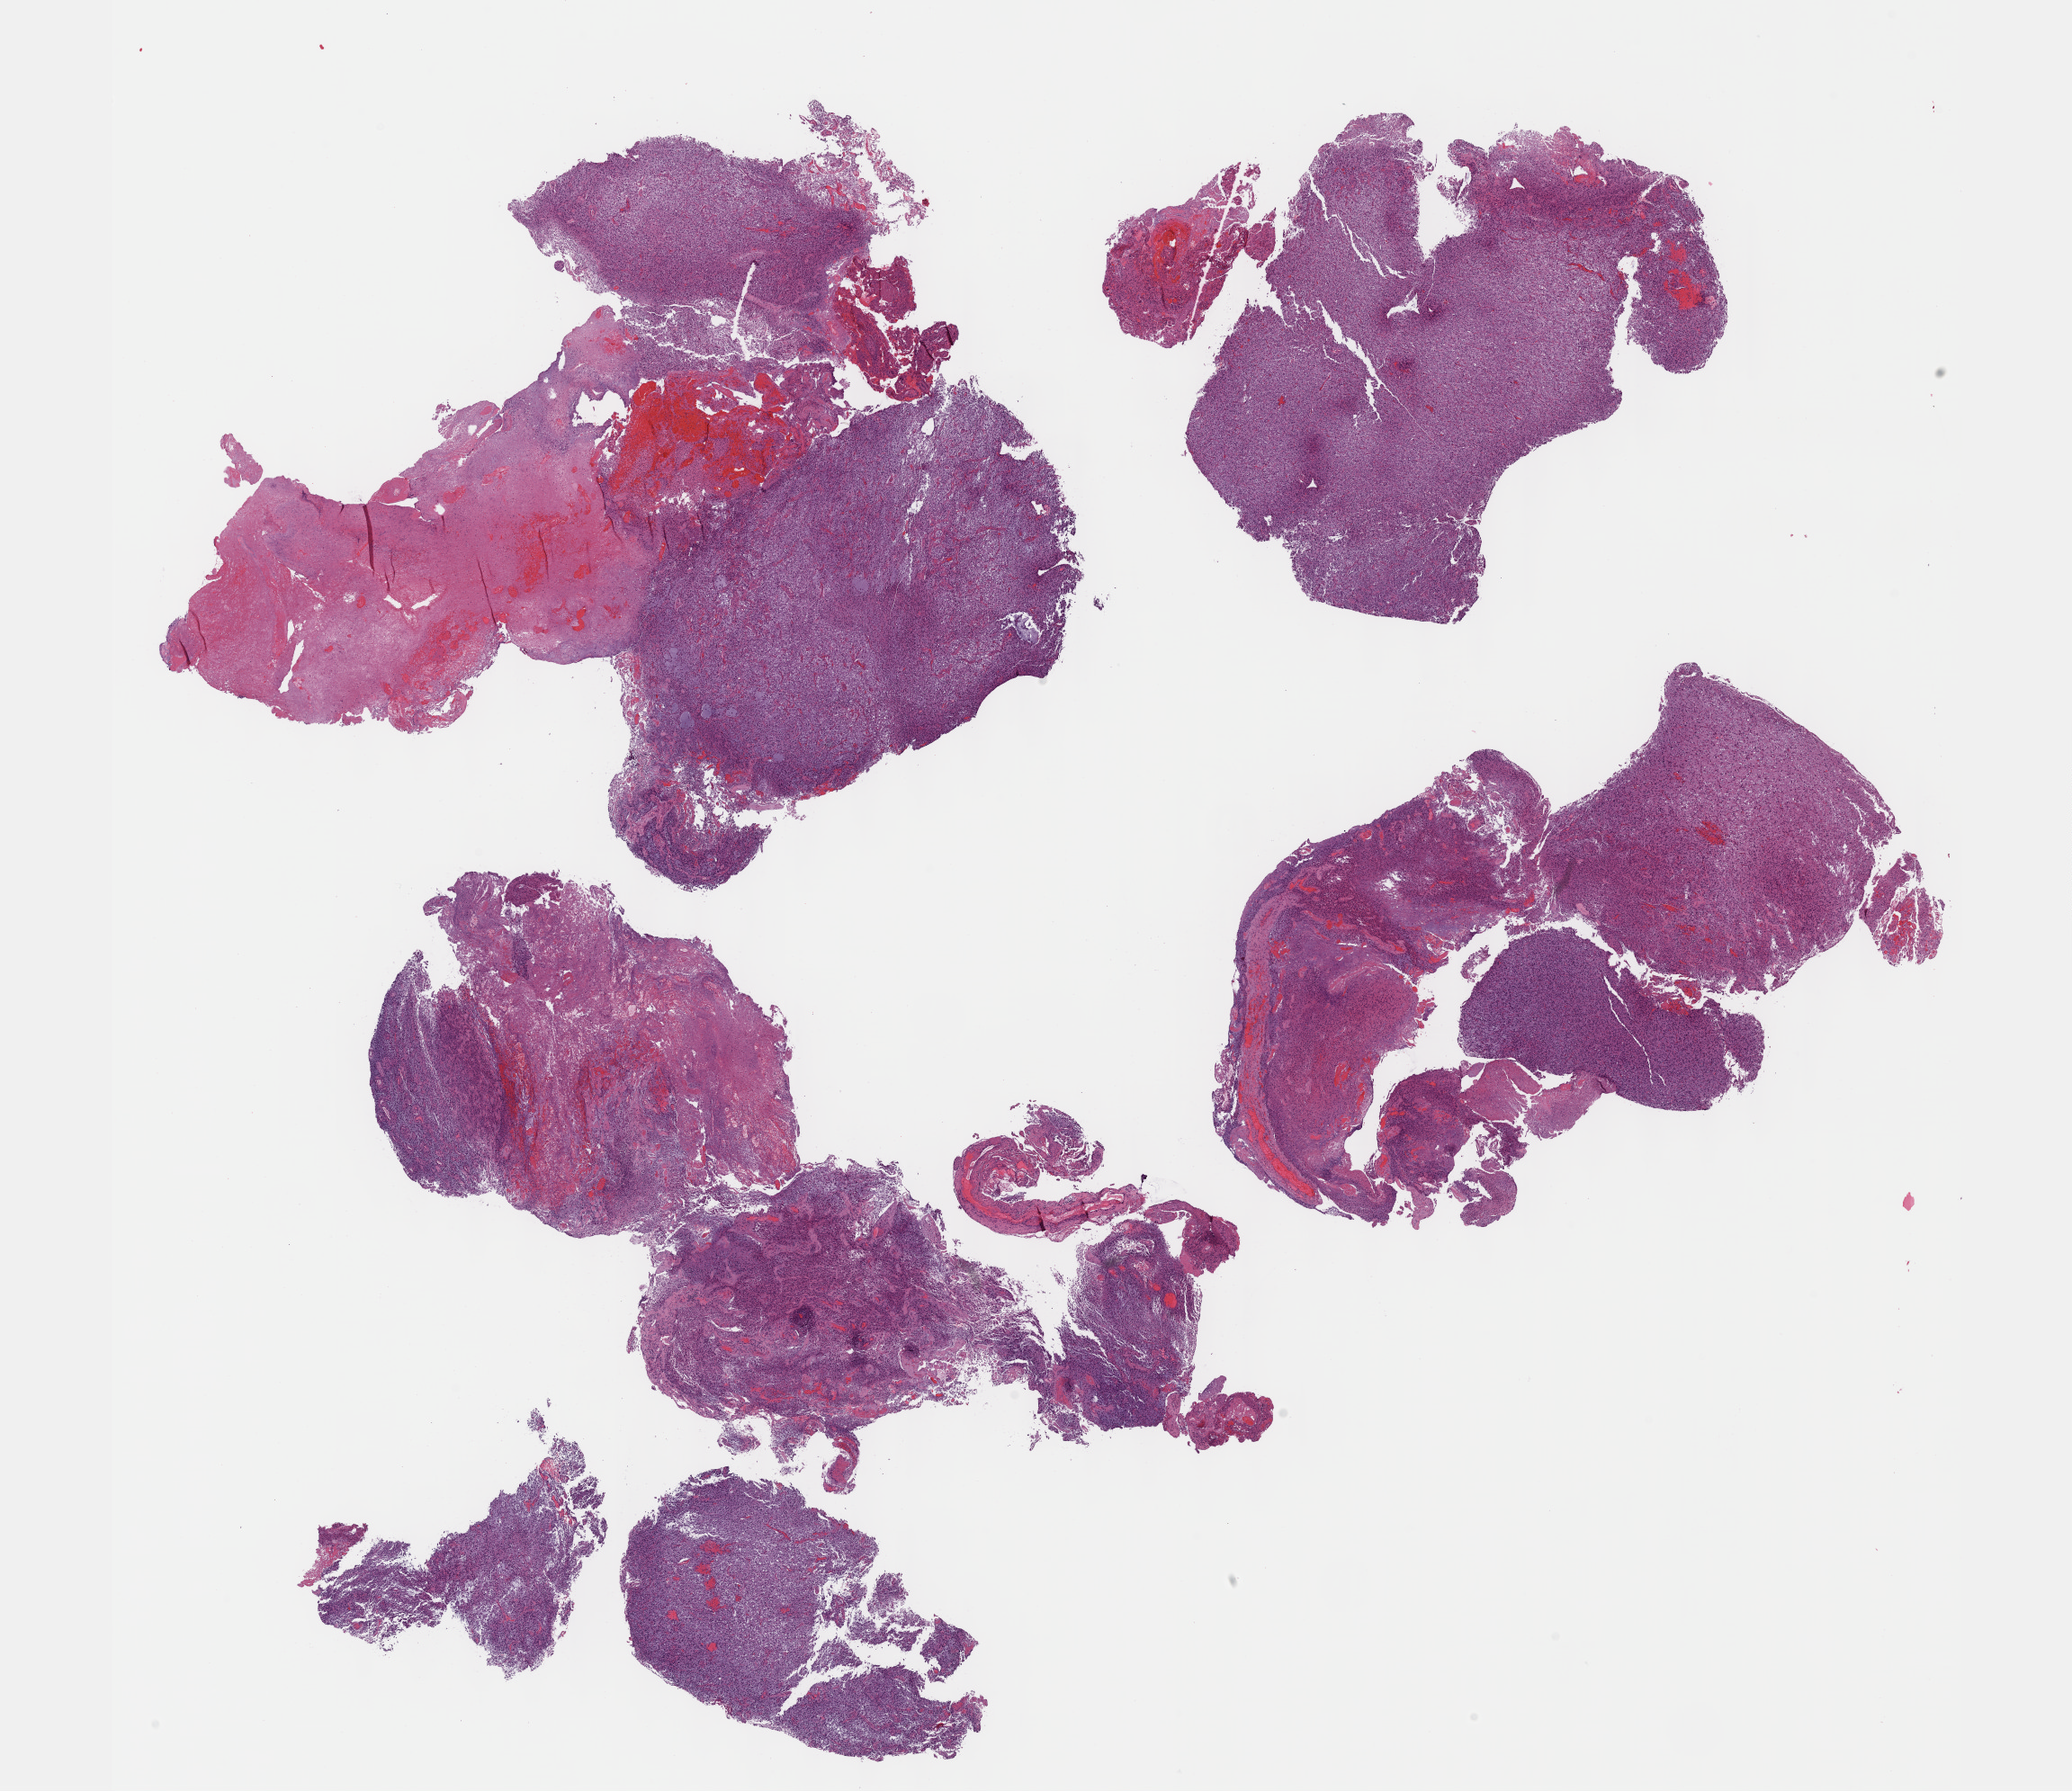
Digitized H&E tissue section (whole slide), low-resolution overview of the scanned area, about 18.6 x 16.1 mm (acquisition: 40x scan); formalin-fixed paraffin-embedded (FFPE) diagnostic section; sample: primary tumour, brain. Male, age 66 years at initial diagnosis. Histologic grade: G3 (poorly differentiated).
Pathologic diagnosis: Oligodendroglioma, anaplastic (cerebrum). Laterality: left.